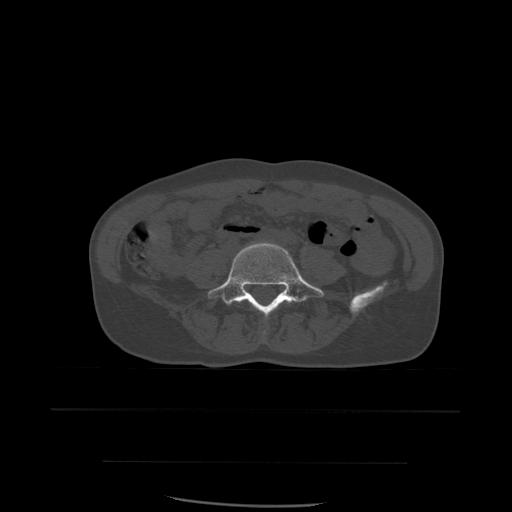
CT including the spine, one axial slice. Slice 153 of 574 in the series (ordered by position). Bone window (W 1800 / L 400 HU). 1.25 mm slice thickness. 512 × 512 image matrix. Patient age 48 years. From the clinical record (not read from this slice): primary cancer: lung; vertebrae with lytic lesions (as recorded): T11.
Annotated regions visible in this slice (semi-automatically segmented with operator editing):
- L4 vertebra: bounding box (x1, y1, x2, y2) in pixels: (237, 301, 242, 304)
- L5 vertebra: (208, 243, 324, 317)